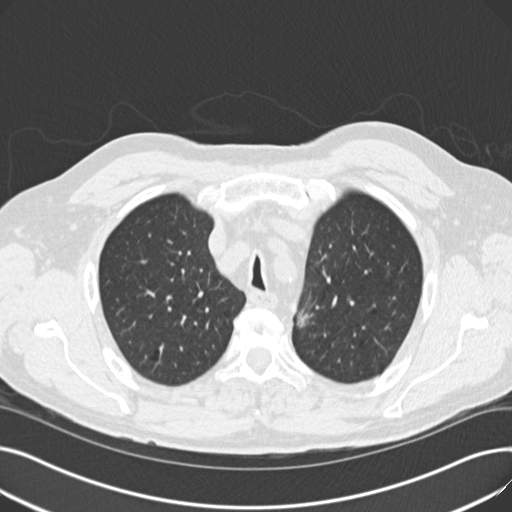
Chest CT (low-dose screening protocol), one axial image. Second screening round (one year after baseline). Lung window (W 1500 / L -600 HU). Slice 45 of 187 in the series. Male, age 70 years at enrolment. Current smoker at enrolment.
• Lesion marked by an expert reader, bounding box [x1, y1, x2, y2] px = [279, 295, 322, 339].
• The screening reader recorded 2 non-calcified nodules or masses ≥4 mm on this exam (left upper lobe, left lower lobe); which of them this box marks is not recorded.
• Participant outcome: lung cancer diagnosed 581 days after this screen — mixed cell adenocarcinoma, left upper lobe, poorly differentiated (G3), stage IIB (AJCC 6th edition), 17 mm at pathology.